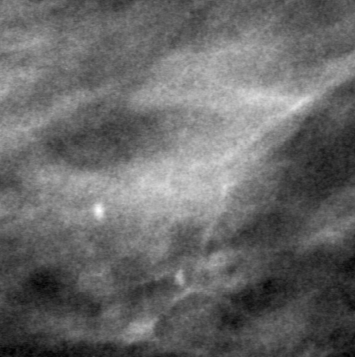
Cropped region of a digitized screen-film mammogram centred on a radiologist-marked abnormality; left breast; MLO view; BI-RADS breast density category 3 (scale 1–4).
- Mass, shape oval, margins circumscribed / obscured; BI-RADS assessment category 4; subtlety rating 4 on a 1 (subtle) to 5 (obvious) scale; pathology (as recorded): benign.